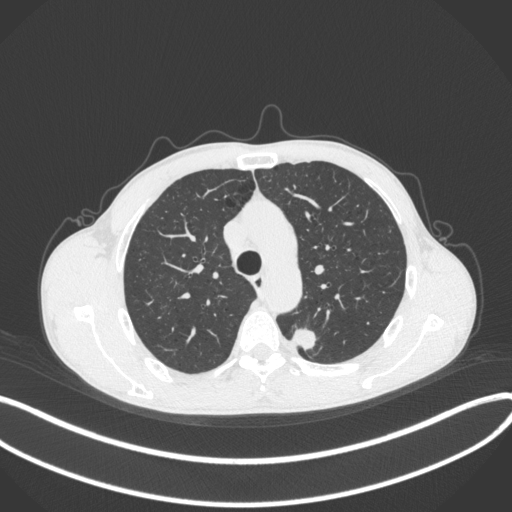
Chest CT, one axial slice. Reconstruction kernel B31f. 120 kVp. Lung window (W 1500 / L -600 HU). 1 mm slice thickness. 512 × 512 image matrix, field of view 400 × 400 mm. Patient: male, 51 years. Case-level facts recorded for this patient, not image findings: clinical TNM (as recorded): T2a N1 M1.
Structures marked on this image (rectangle marked by the reading radiologist):
- lung tumour (recorded histology: adenocarcinoma): bounding box (x1, y1, x2, y2) in pixels: (290, 325, 321, 356)